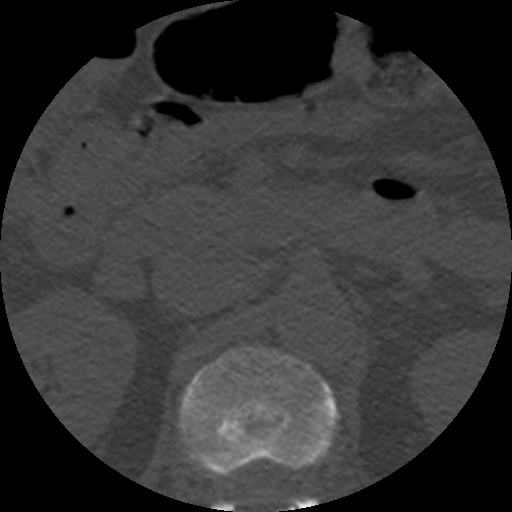
CT including the spine, one axial slice. Position 197 of 508 along the scan axis. 120 kVp. Bone window (W 1800 / L 400 HU). 1.25 mm slice thickness. 512 × 512 image matrix, field of view 160 × 160 mm. Patient age 57 years. From the clinical record (not read from this slice): primary cancer: prostate.
Annotated regions visible in this slice (semi-automatic segmentation, software-assisted and operator-edited):
- L1 vertebra: bounding box (x1, y1, x2, y2) in pixels: (179, 346, 338, 512)